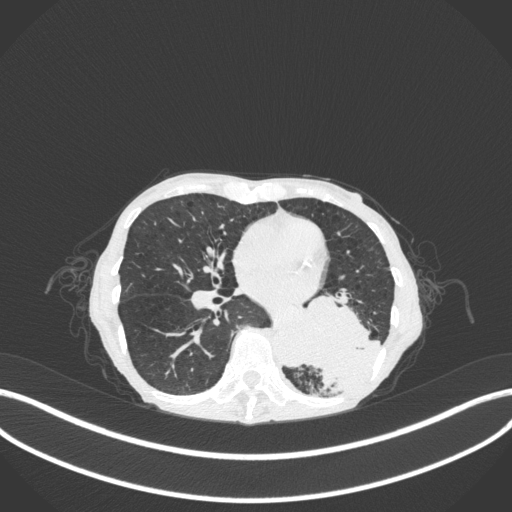
Chest CT, one axial slice; slice 124 of 347 in the series (ordered by position); reconstruction kernel B31f; 120 kVp; lung window (W 1500 / L -600 HU); 1 mm slice thickness; 512 × 512 image matrix, field of view 400 × 400 mm. Patient: female, 70 years. From the clinical record (not read from this slice): clinical TNM (as recorded): T3 N0 M0.
Annotated regions visible in this slice (rectangle marked by the reading radiologist):
- lung tumour (recorded histology: small cell carcinoma): box from (x=290, y=278) to (x=379, y=392) px